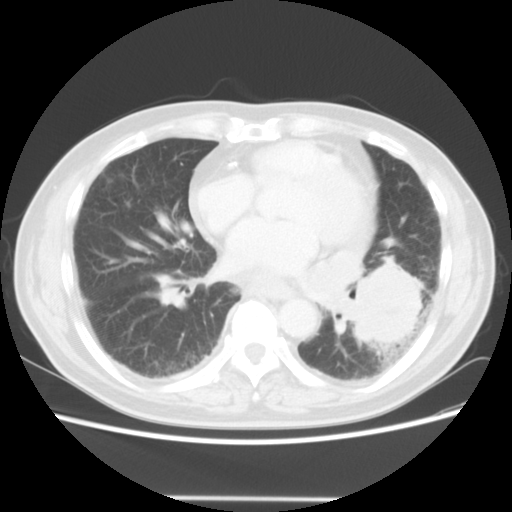
Chest CT, one axial slice. Position 20 of 56 along the scan axis. Reconstruction kernel STANDARD. Lung window (W 1500 / L -600 HU). 512 × 512 image matrix, field of view 360 × 360 mm. Male patient, age 66 years. From the clinical record (not read from this slice): clinical TNM (as recorded): T4 N3 M0.
Outlined on this slice (rectangle marked by the reading radiologist):
- lung tumour (recorded histology: small cell carcinoma): bounding box <339,256,434,346> (left, top, right, bottom; pixels)